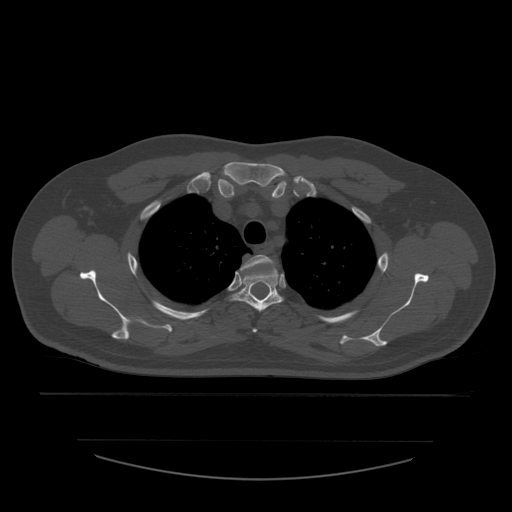
CT including the spine, one axial slice; slice 437 of 532 in the series (ordered by position); reconstruction kernel STANDARD; bone window (W 1800 / L 400 HU); 1.25 mm slice thickness; 512 × 512 image matrix, field of view 441 × 441 mm. Patient age 44 years. From the clinical record (not read from this slice): primary cancer: soft tissue sarcoma.
Annotated regions visible in this slice (semi-automatic segmentation, software-assisted and operator-edited):
- T2 vertebra: bounding box [x1, y1, x2, y2] px = [241, 255, 275, 333]
- T3 vertebra: [232, 263, 283, 312]